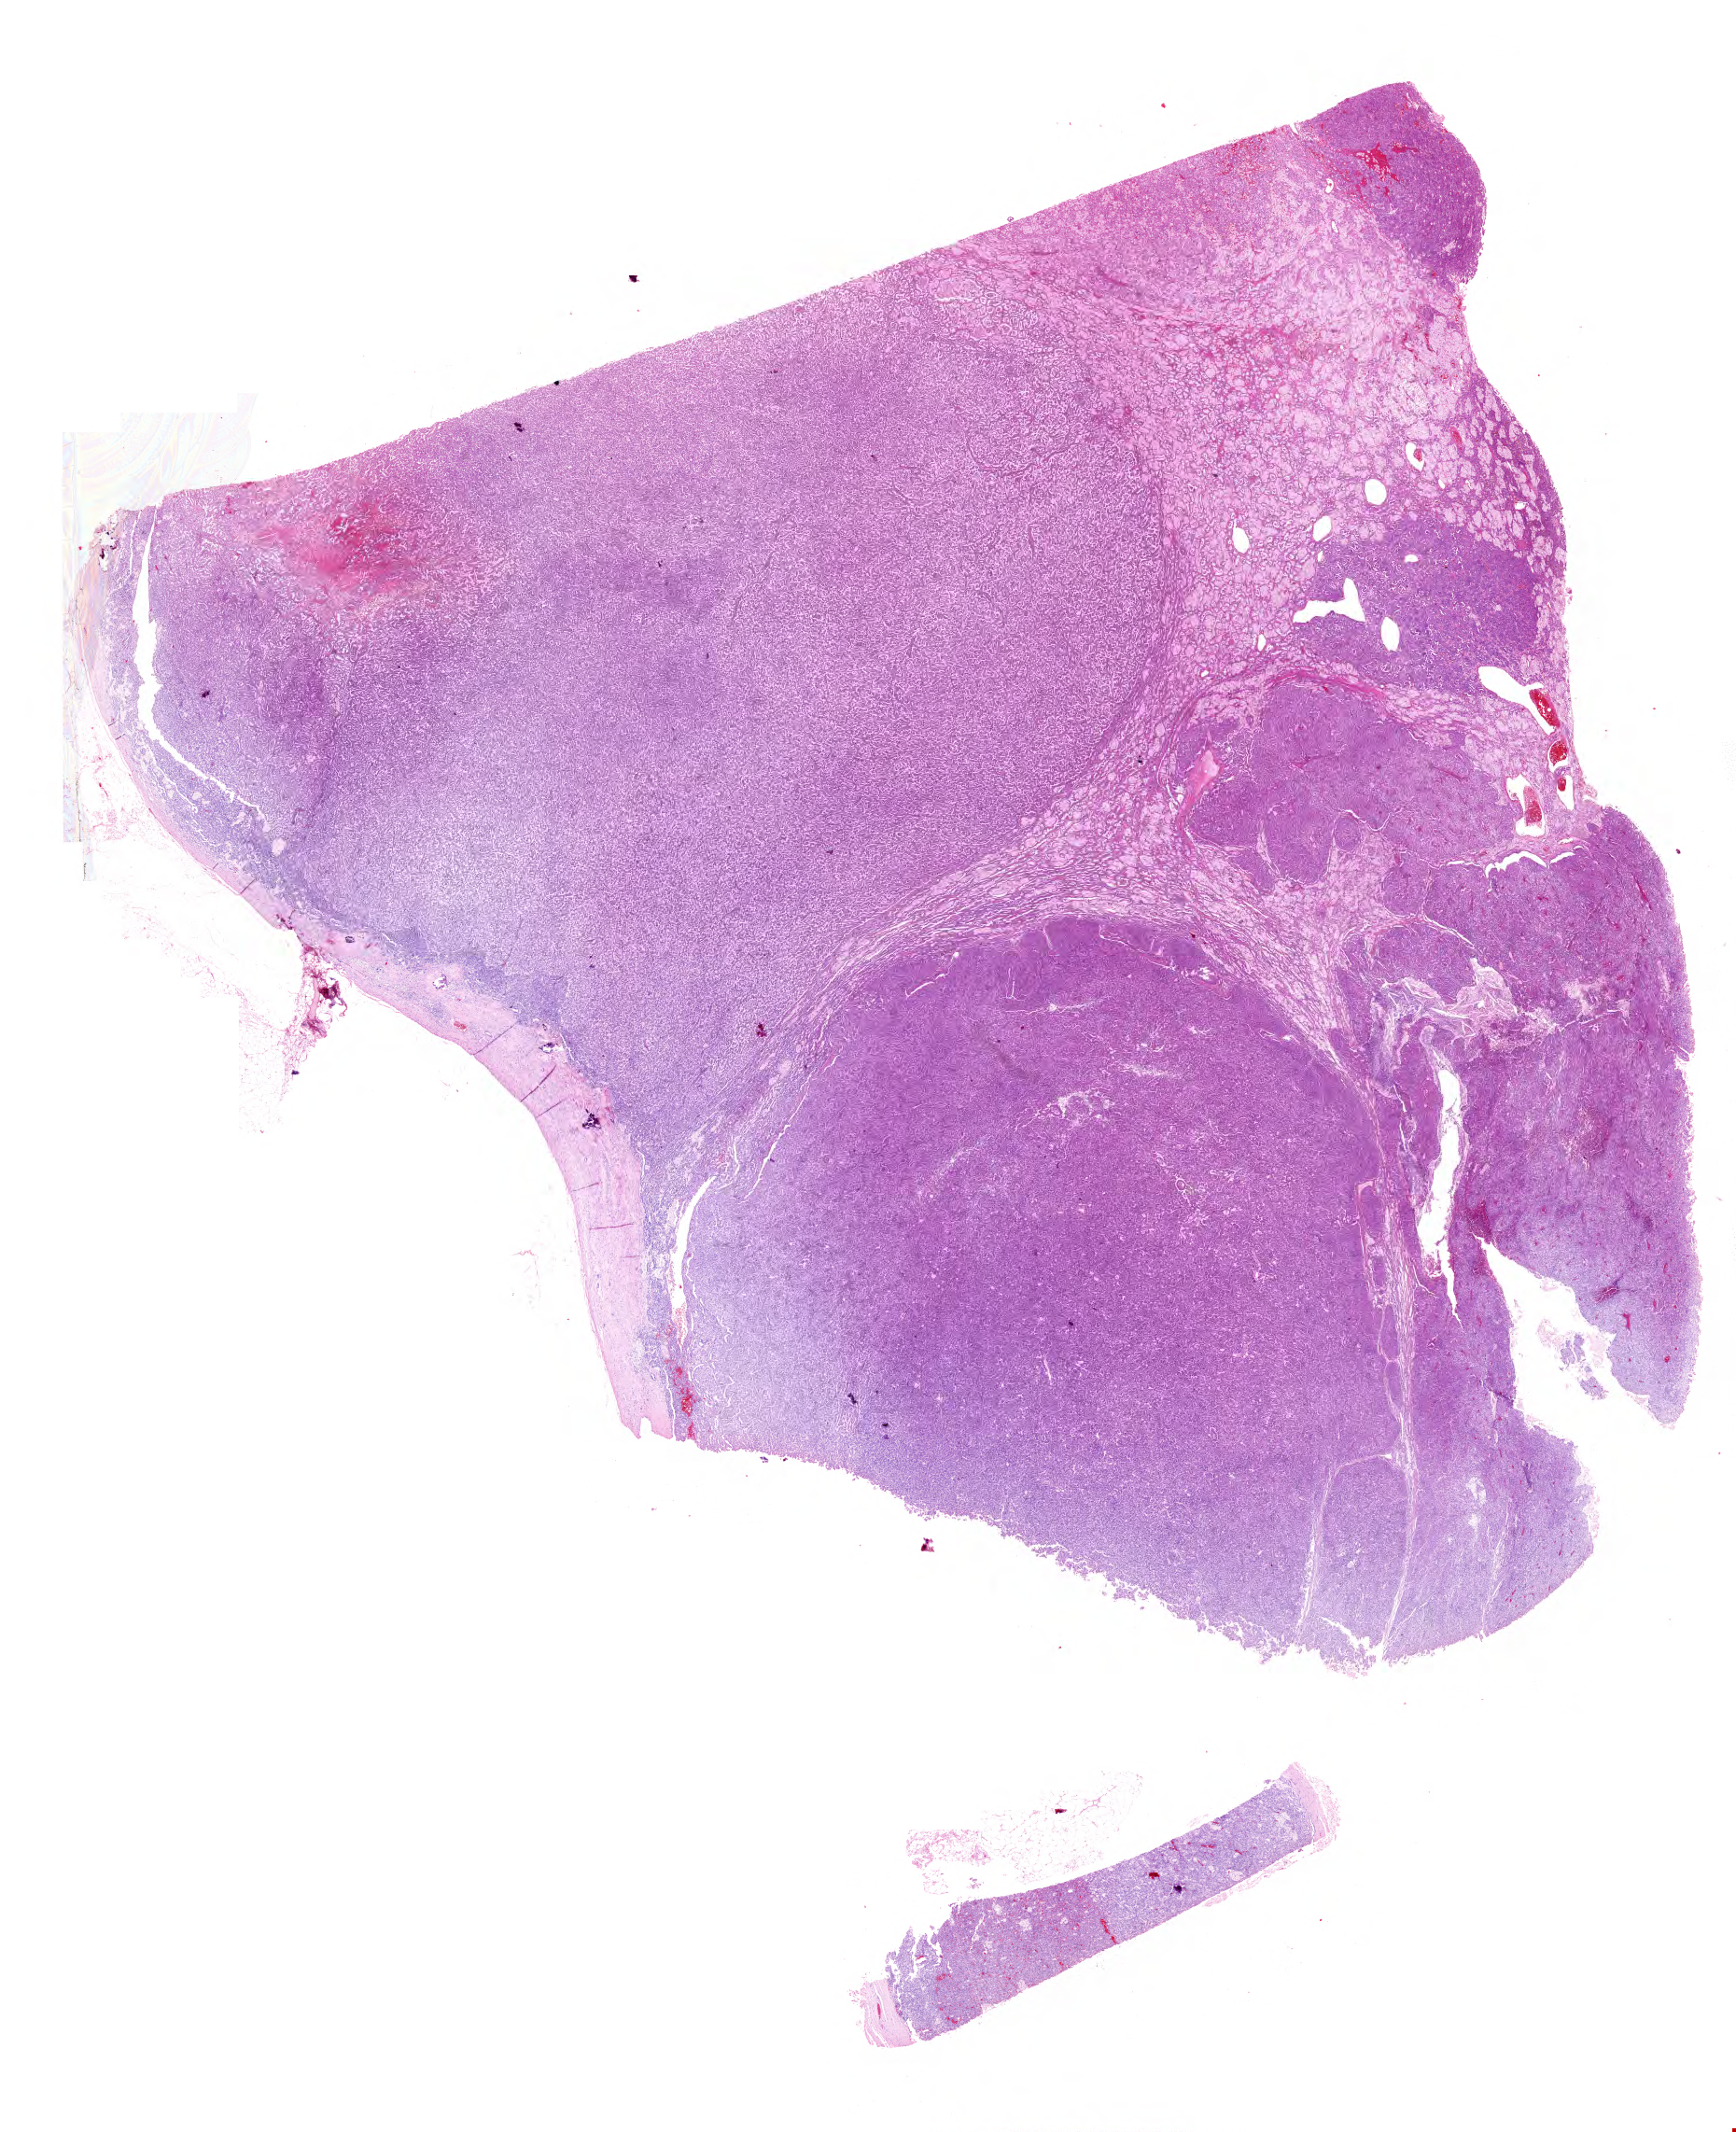
Whole-slide histology image, H&E-stained — low-resolution overview of the scanned area, about 23.2 x 28.4 mm (from a 40x scan); formalin-fixed paraffin-embedded (FFPE) diagnostic section; primary tumour sample from the kidney. Patient: male, age at initial diagnosis 54 years.
Pathologic diagnosis: Papillary adenocarcinoma, NOS.